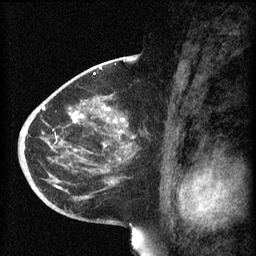
Breast MRI (dynamic contrast-enhanced), one sagittal slice. Slice 36 of 60 in the series (ordered by position). 3 images stored at this slice position (order not interpretable as contrast timing). 1.5 T. TE 4.2 ms, TR 8.1 ms. 2 mm slice thickness. 256 × 256 image matrix, field of view 200 × 200 mm. Female patient, age 44 years.
Structures marked on this image (semi-automatically segmented with operator editing):
- analysis volume of interest (the breast-tissue region the enhancement analysis was run in; not a lesion): bounding box [x1, y1, x2, y2] px = [59, 110, 147, 169]
- tumour enhancement mask (voxels above the 70 % enhancement threshold inside the analysis volume of interest): [72, 110, 128, 151]